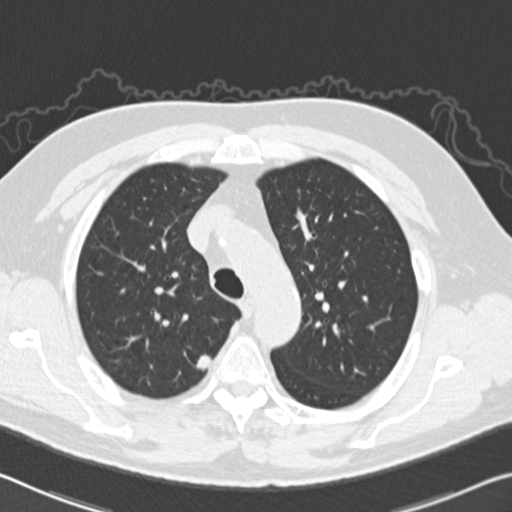
Chest CT (low-dose screening protocol), one axial image. Baseline screening round. Lung window (W 1500 / L -600 HU). 120 kVp. Male participant, aged 64 years at enrolment. Former smoker at enrolment.
Expert reader's lesion annotation, box from (x=184, y=343) to (x=228, y=385) px. Screening reader's record for this exam (one nodule recorded; not confirmed to be the boxed lesion): non-calcified nodule or mass ≥4 mm, right upper lobe, 10 × 8 mm, spiculated (stellate) margins, soft tissue attenuation. Lung cancer was diagnosed 99 days after this screen: adenocarcinoma, NOS, right upper lobe, poorly differentiated (G3), stage IA (AJCC 6th edition), 11 mm at pathology.